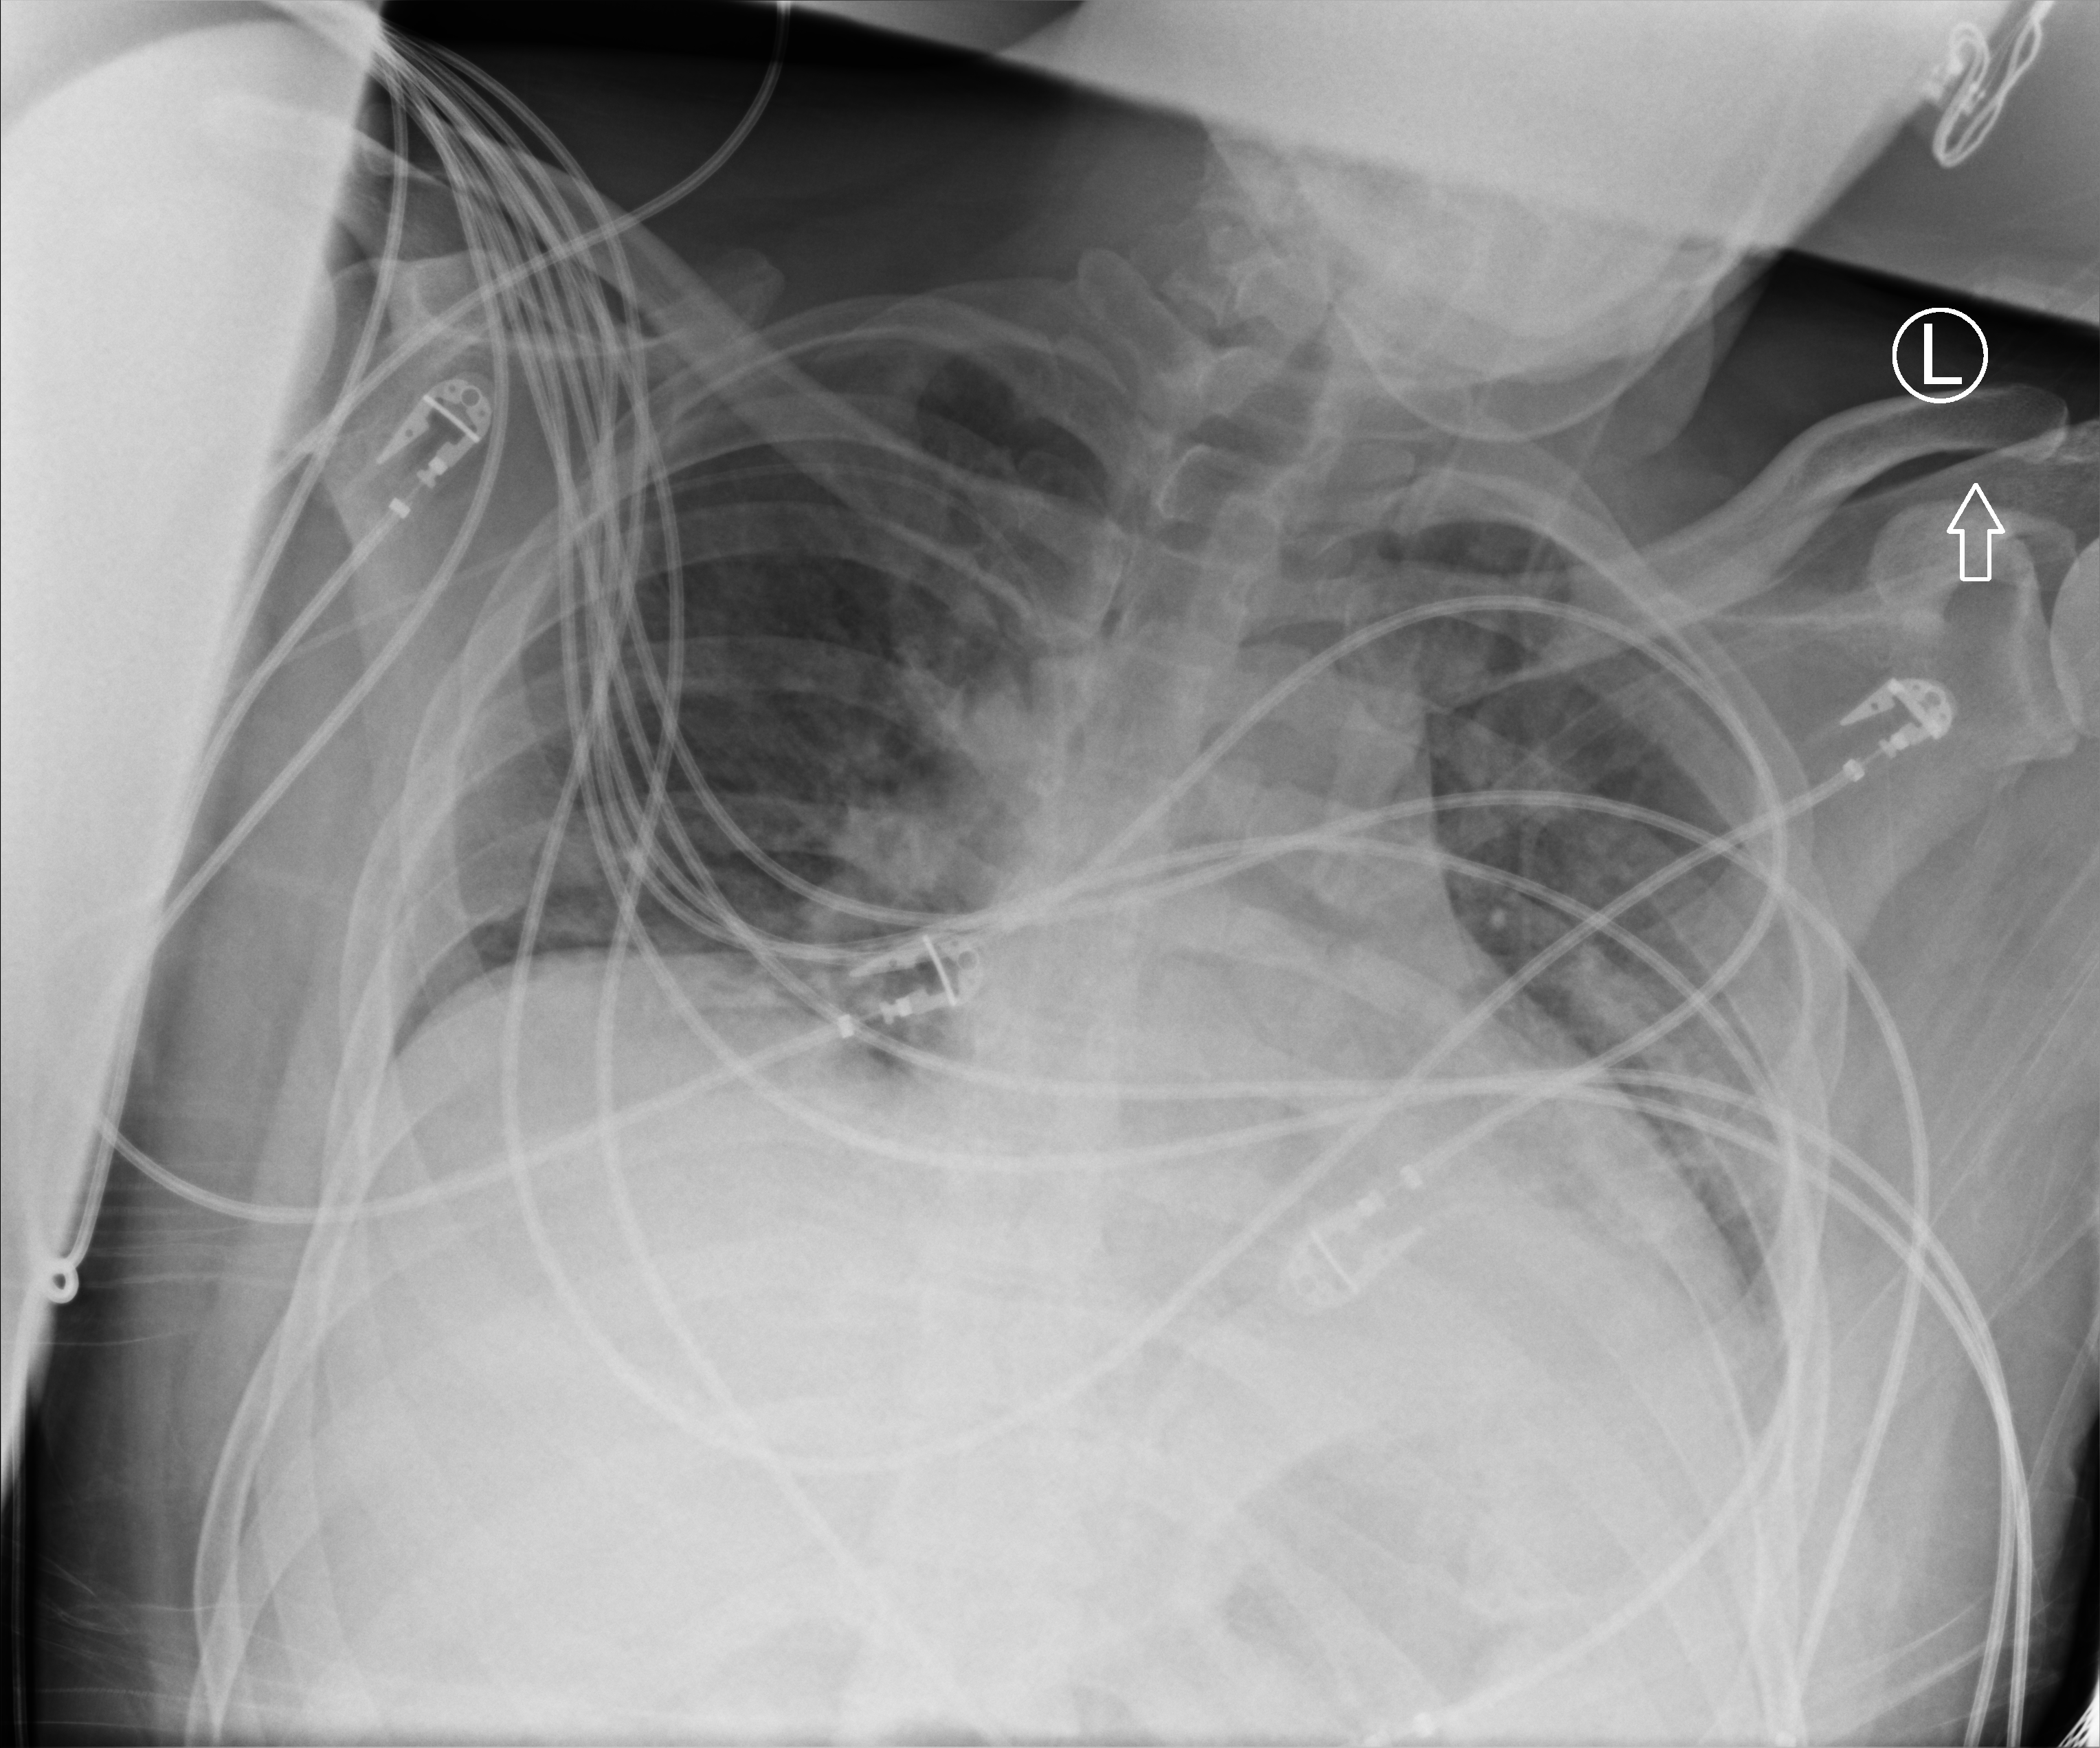
Bedside chest radiograph (computed radiography); anteroposterior (AP) projection. Patient hospitalised with COVID-19; male, aged 18–59 years.
Hospital-stay facts (about this admission, not read from this image; timing relative to this image not recorded): diabetes (admission record): no.